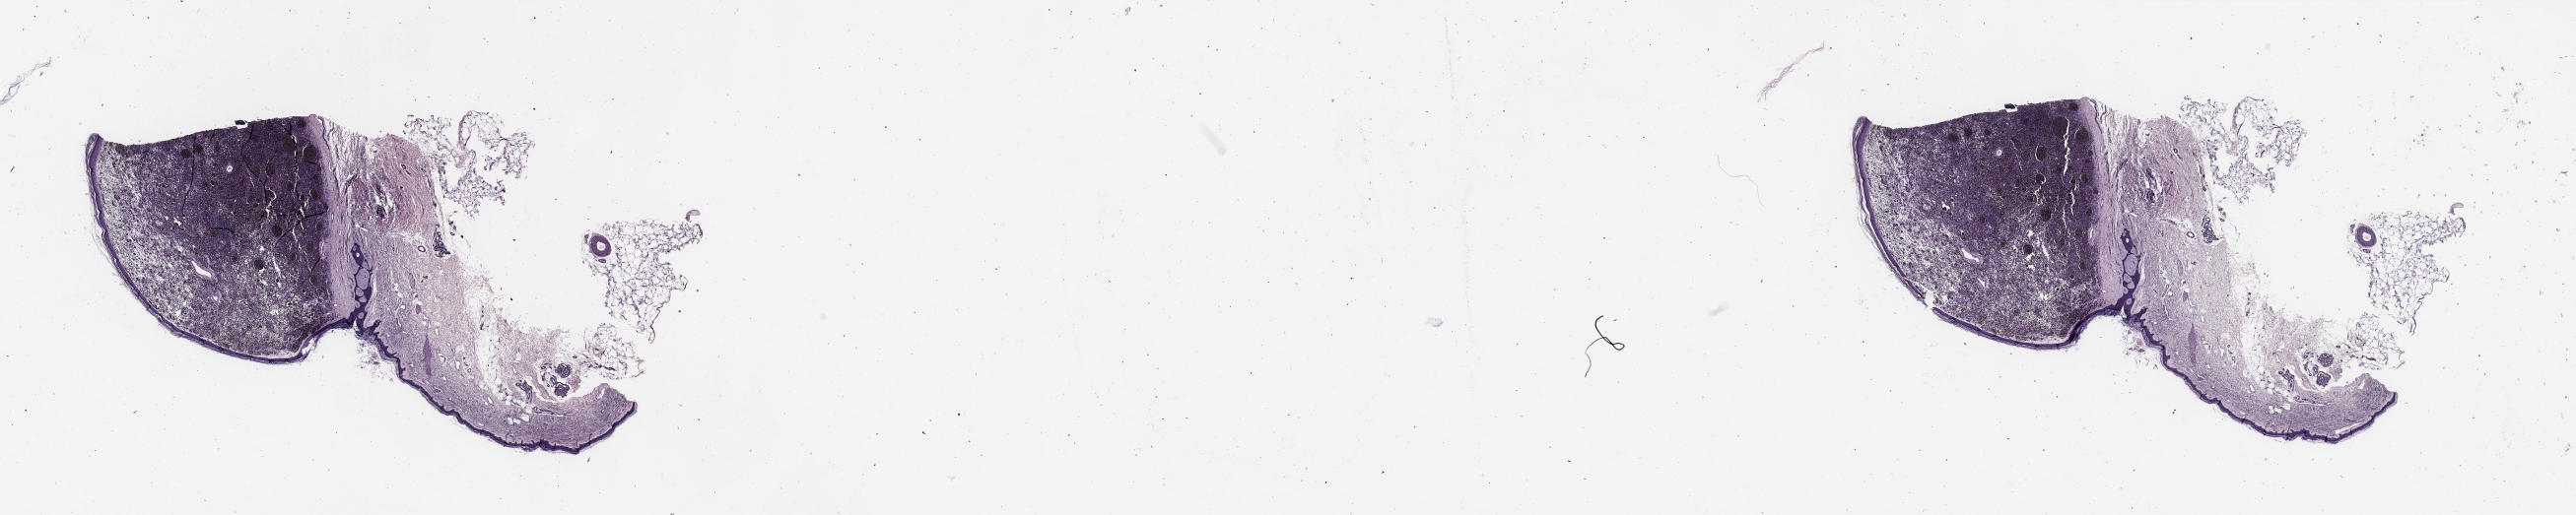
H&E whole-slide image, a low-resolution overview of the entire scanned area, about 41.3 x 8.3 mm. Tumour tissue sample, sampled site: skin. Patient: female, age 78 years. Slide review estimates, as recorded: tumour nuclei 80%, necrosis 0%.
Primary tumour site (as recorded): extremities. AJCC pathologic stage: IIB. Diagnosis: Malignant melanoma, NOS.